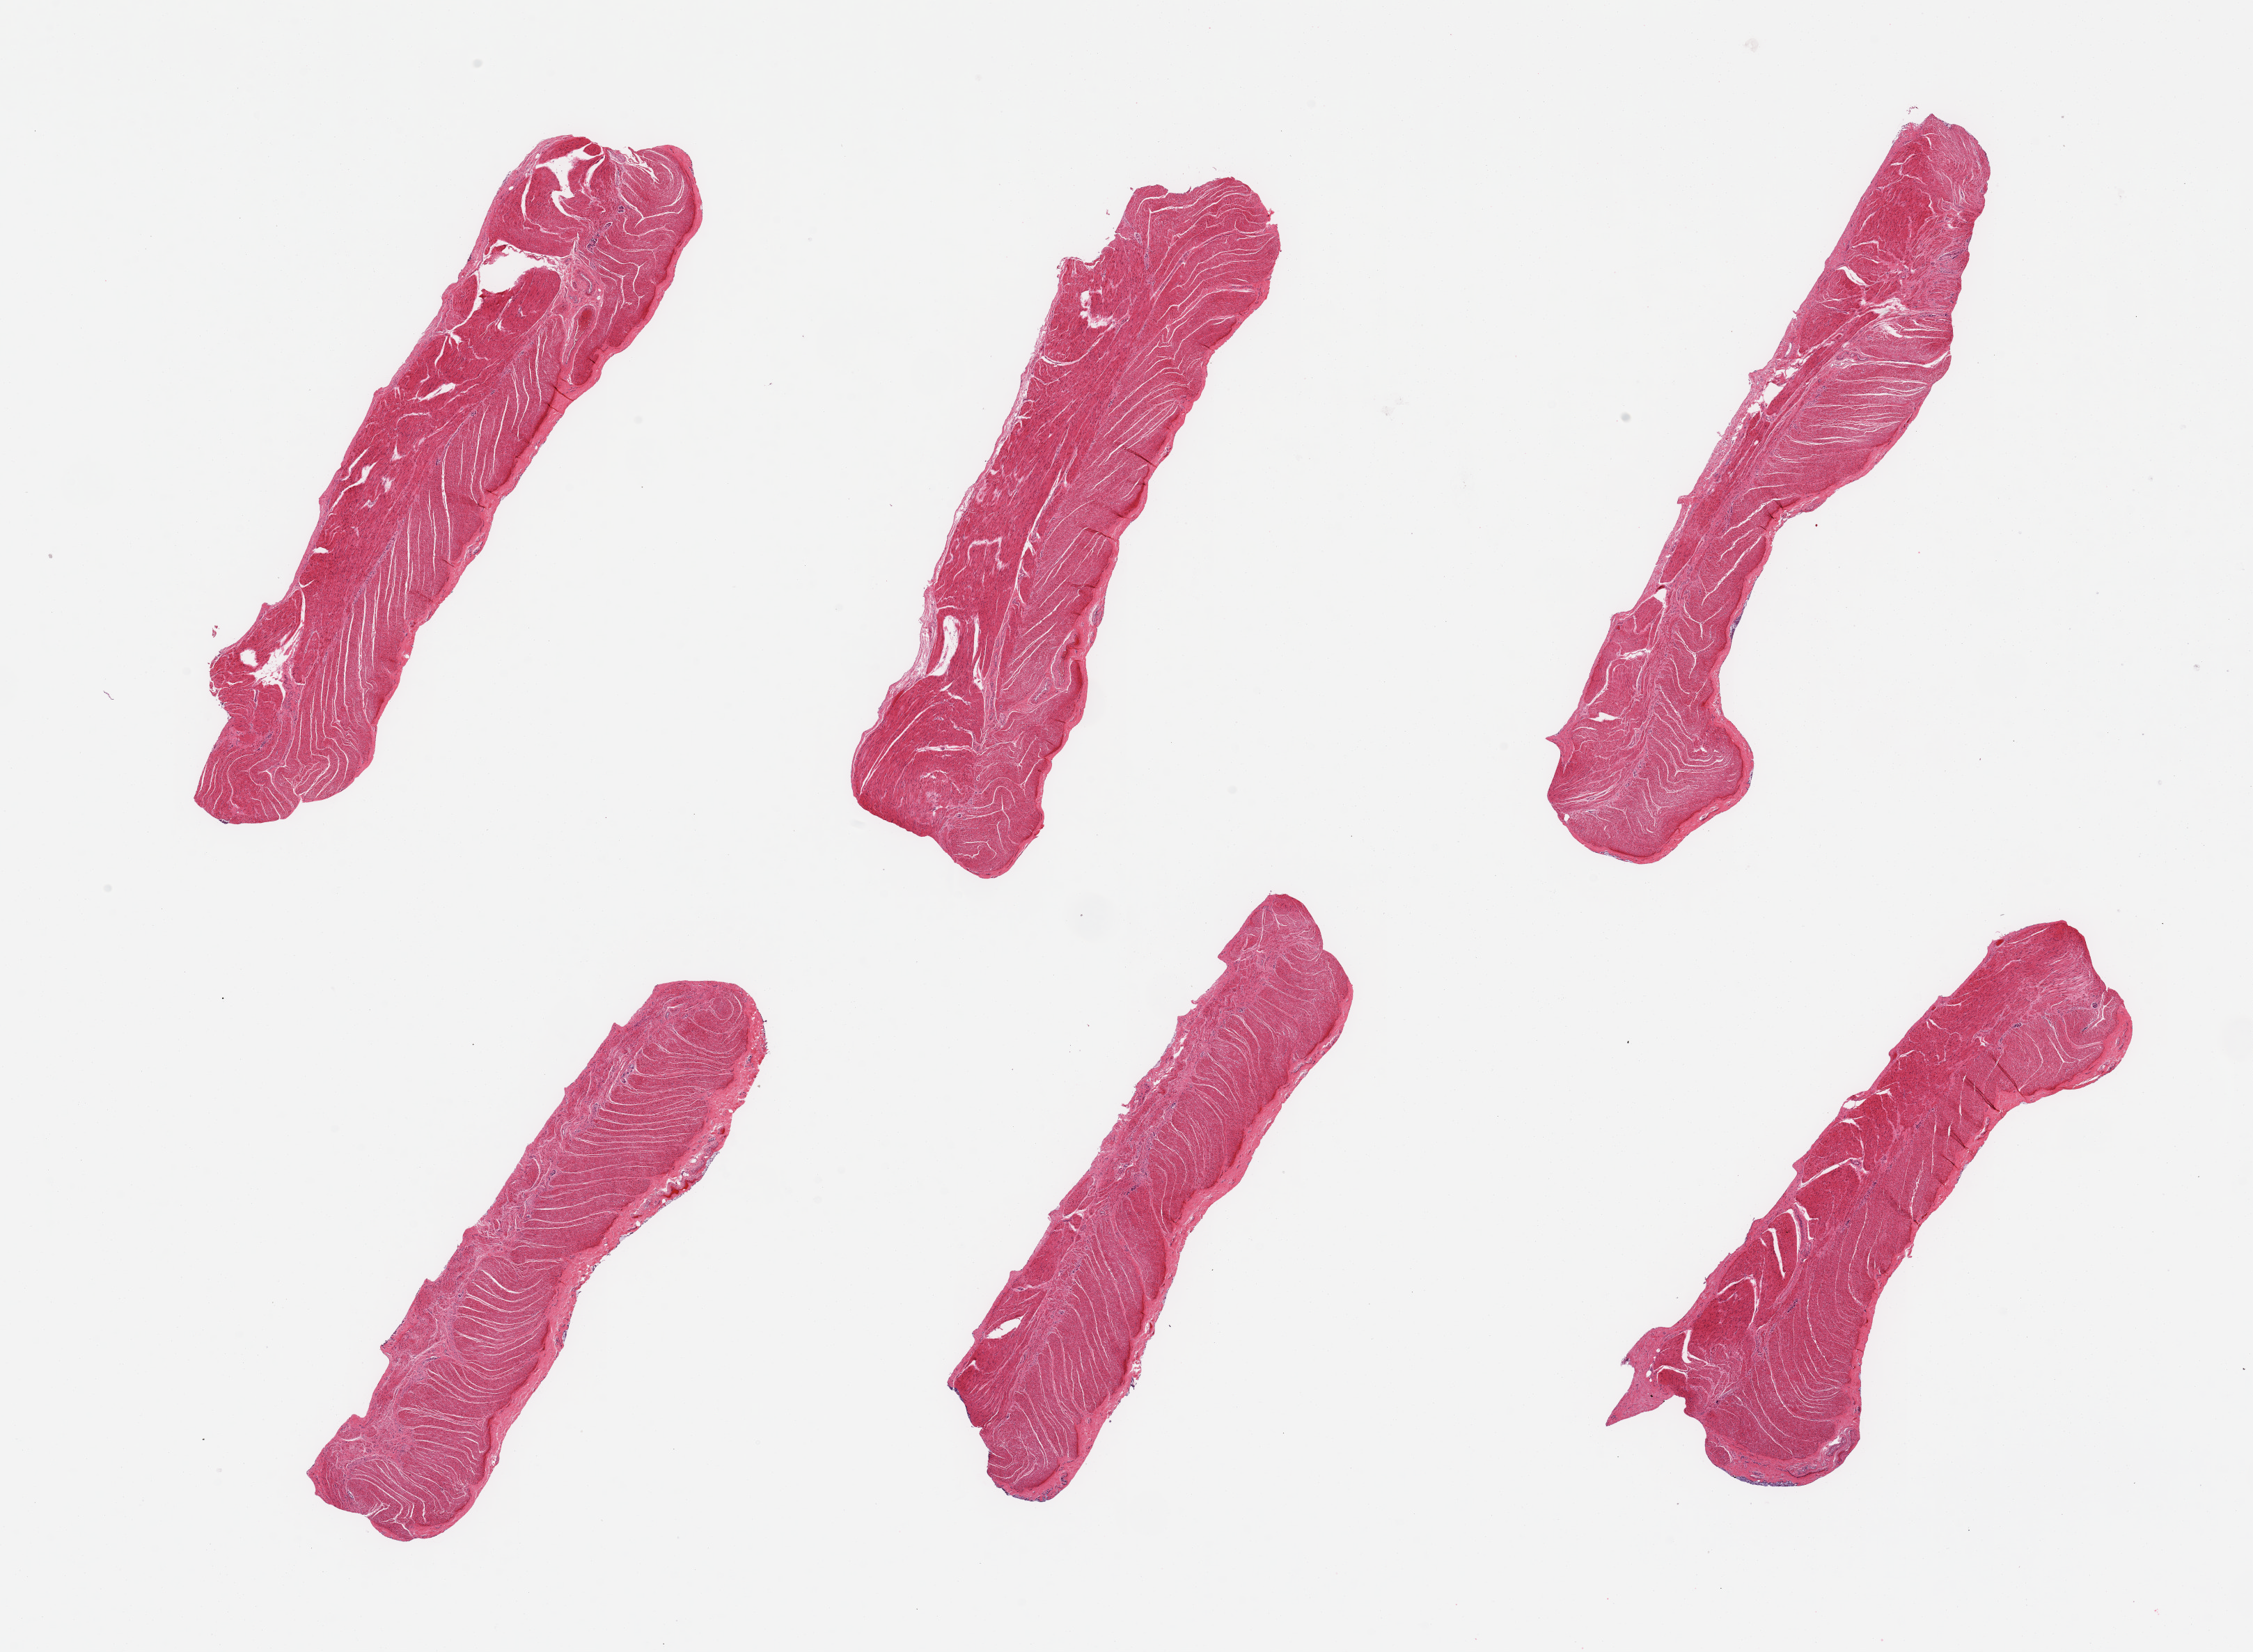
Whole-slide image, hematoxylin and eosin (H&E) stain — whole scanned area (about 25.6 x 18.8 mm) shown as a low-resolution overview; PAXgene-fixed, paraffin-embedded tissue; sampled site (target tissue): sigmoid colon; tissue donor sample.
Pathologist's review note for this sample: 6 pieces, confirmed target muscularis.